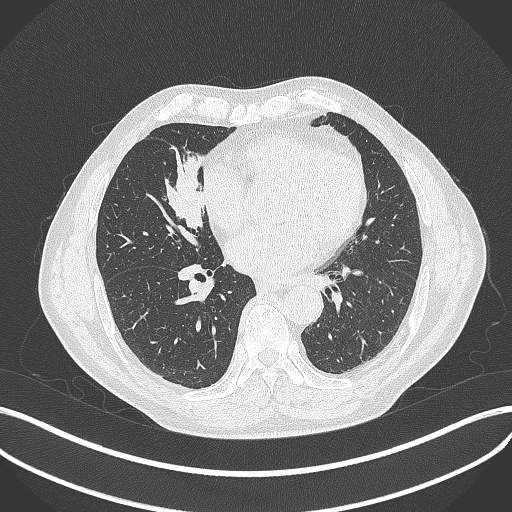
Chest CT, one axial slice. Position 173 of 429 along the scan axis. Reconstruction kernel B70f. Lung window (W 1500 / L -600 HU). 1 mm slice thickness. 512 × 512 image matrix. Male patient, age 61 years. From the clinical record (not read from this slice): clinical TNM (as recorded): T2b N1 M0.
Annotated regions visible in this slice (rectangle marked by the reading radiologist):
- lung tumour (recorded histology: squamous cell carcinoma): bounding box (x1, y1, x2, y2) in pixels: (166, 148, 212, 232)